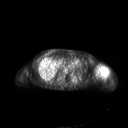
FDG PET of an extremity soft-tissue mass (from a PET/CT study), one axial slice; slice 142 of 267 in the series (ordered by position); 3.27 mm slice thickness; 128 × 128 image matrix, field of view 700 × 700 mm. Female patient, age 83 years. Case-level facts recorded for this patient, not image findings: histological type: pleiomorphic leiomyosarcoma; grade: high; site of the primary tumour: left biceps.
Outlined on this slice (expert contour drawn on MRI and transferred to this co-registered scan by the dataset authors):
- gross tumour volume including surrounding oedema: bounding box (x1, y1, x2, y2) in pixels: (96, 66, 108, 76)
- gross tumour volume (mass): (96, 66, 107, 74)